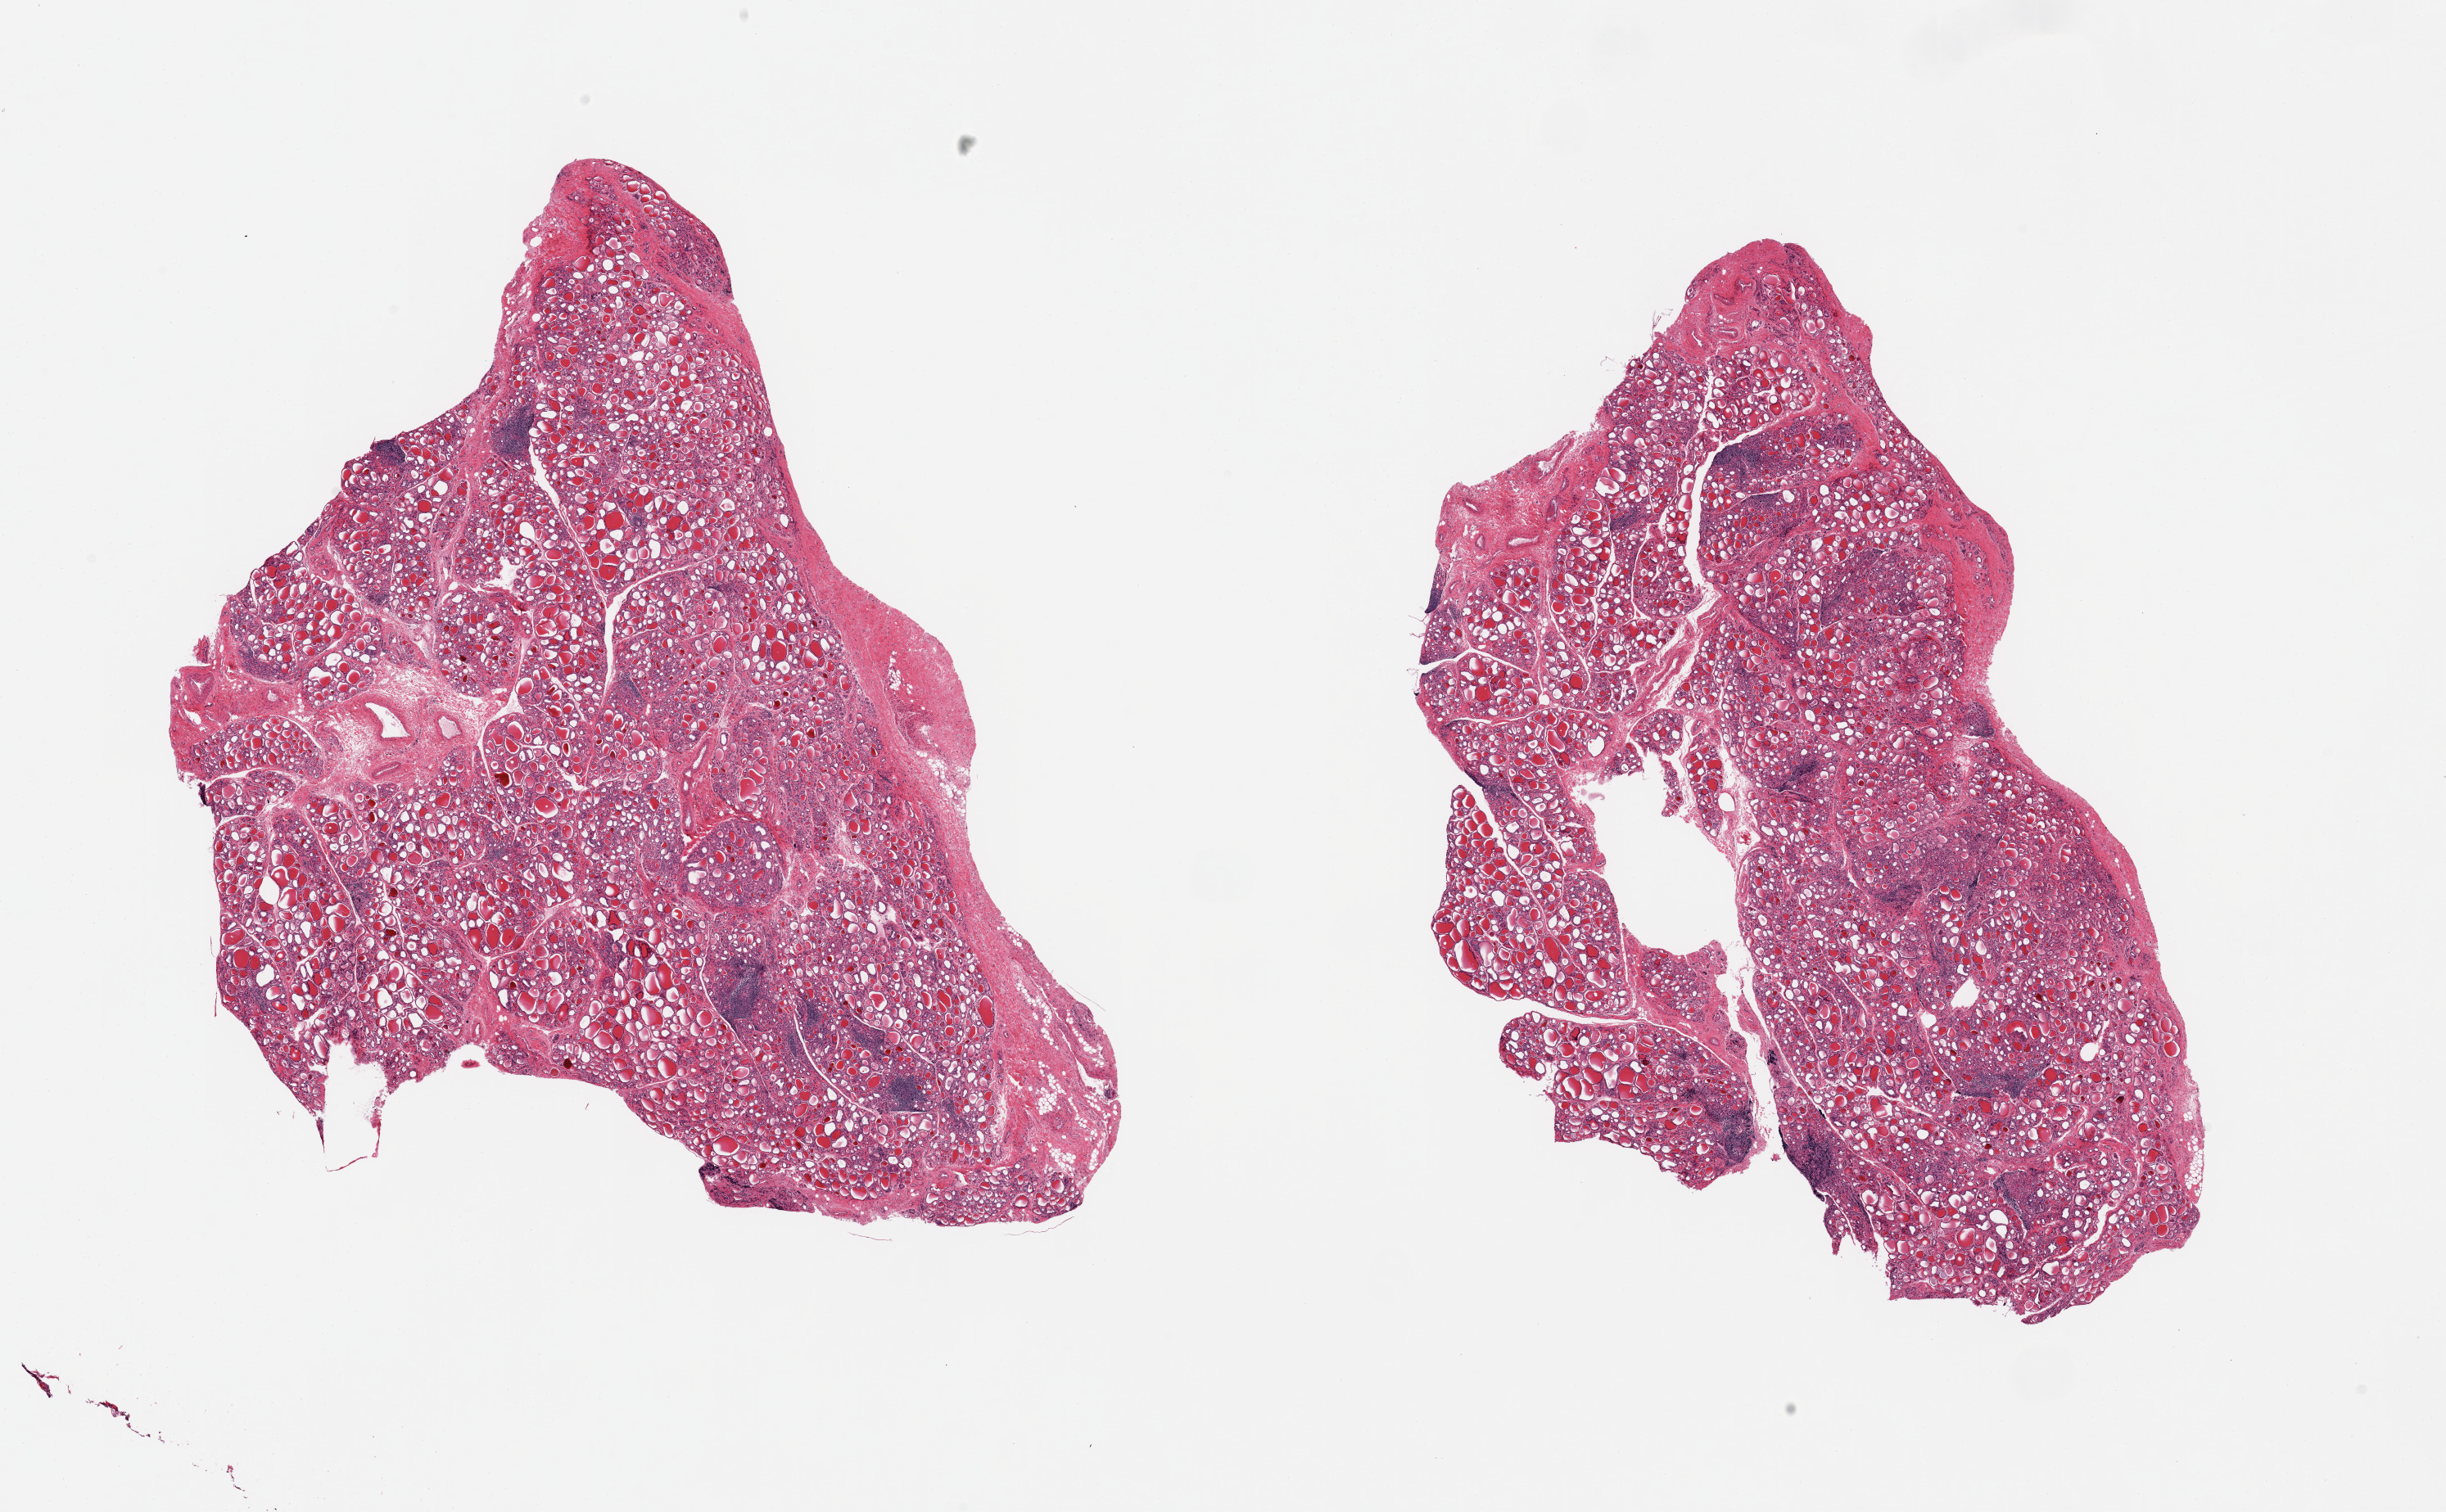
H&E whole-slide image, whole scanned area (about 23.6 x 14.6 mm, slide scanned at 20x) shown as a low-resolution overview, PAXgene-fixed, paraffin-embedded tissue, sampled site (target tissue): thyroid, tissue donor sample. Female donor.
Review note (as recorded): 2 pieces; some fibrosis and nodularity with lymphocytic aggregates, c/w Hashimoto's thyroiditis.